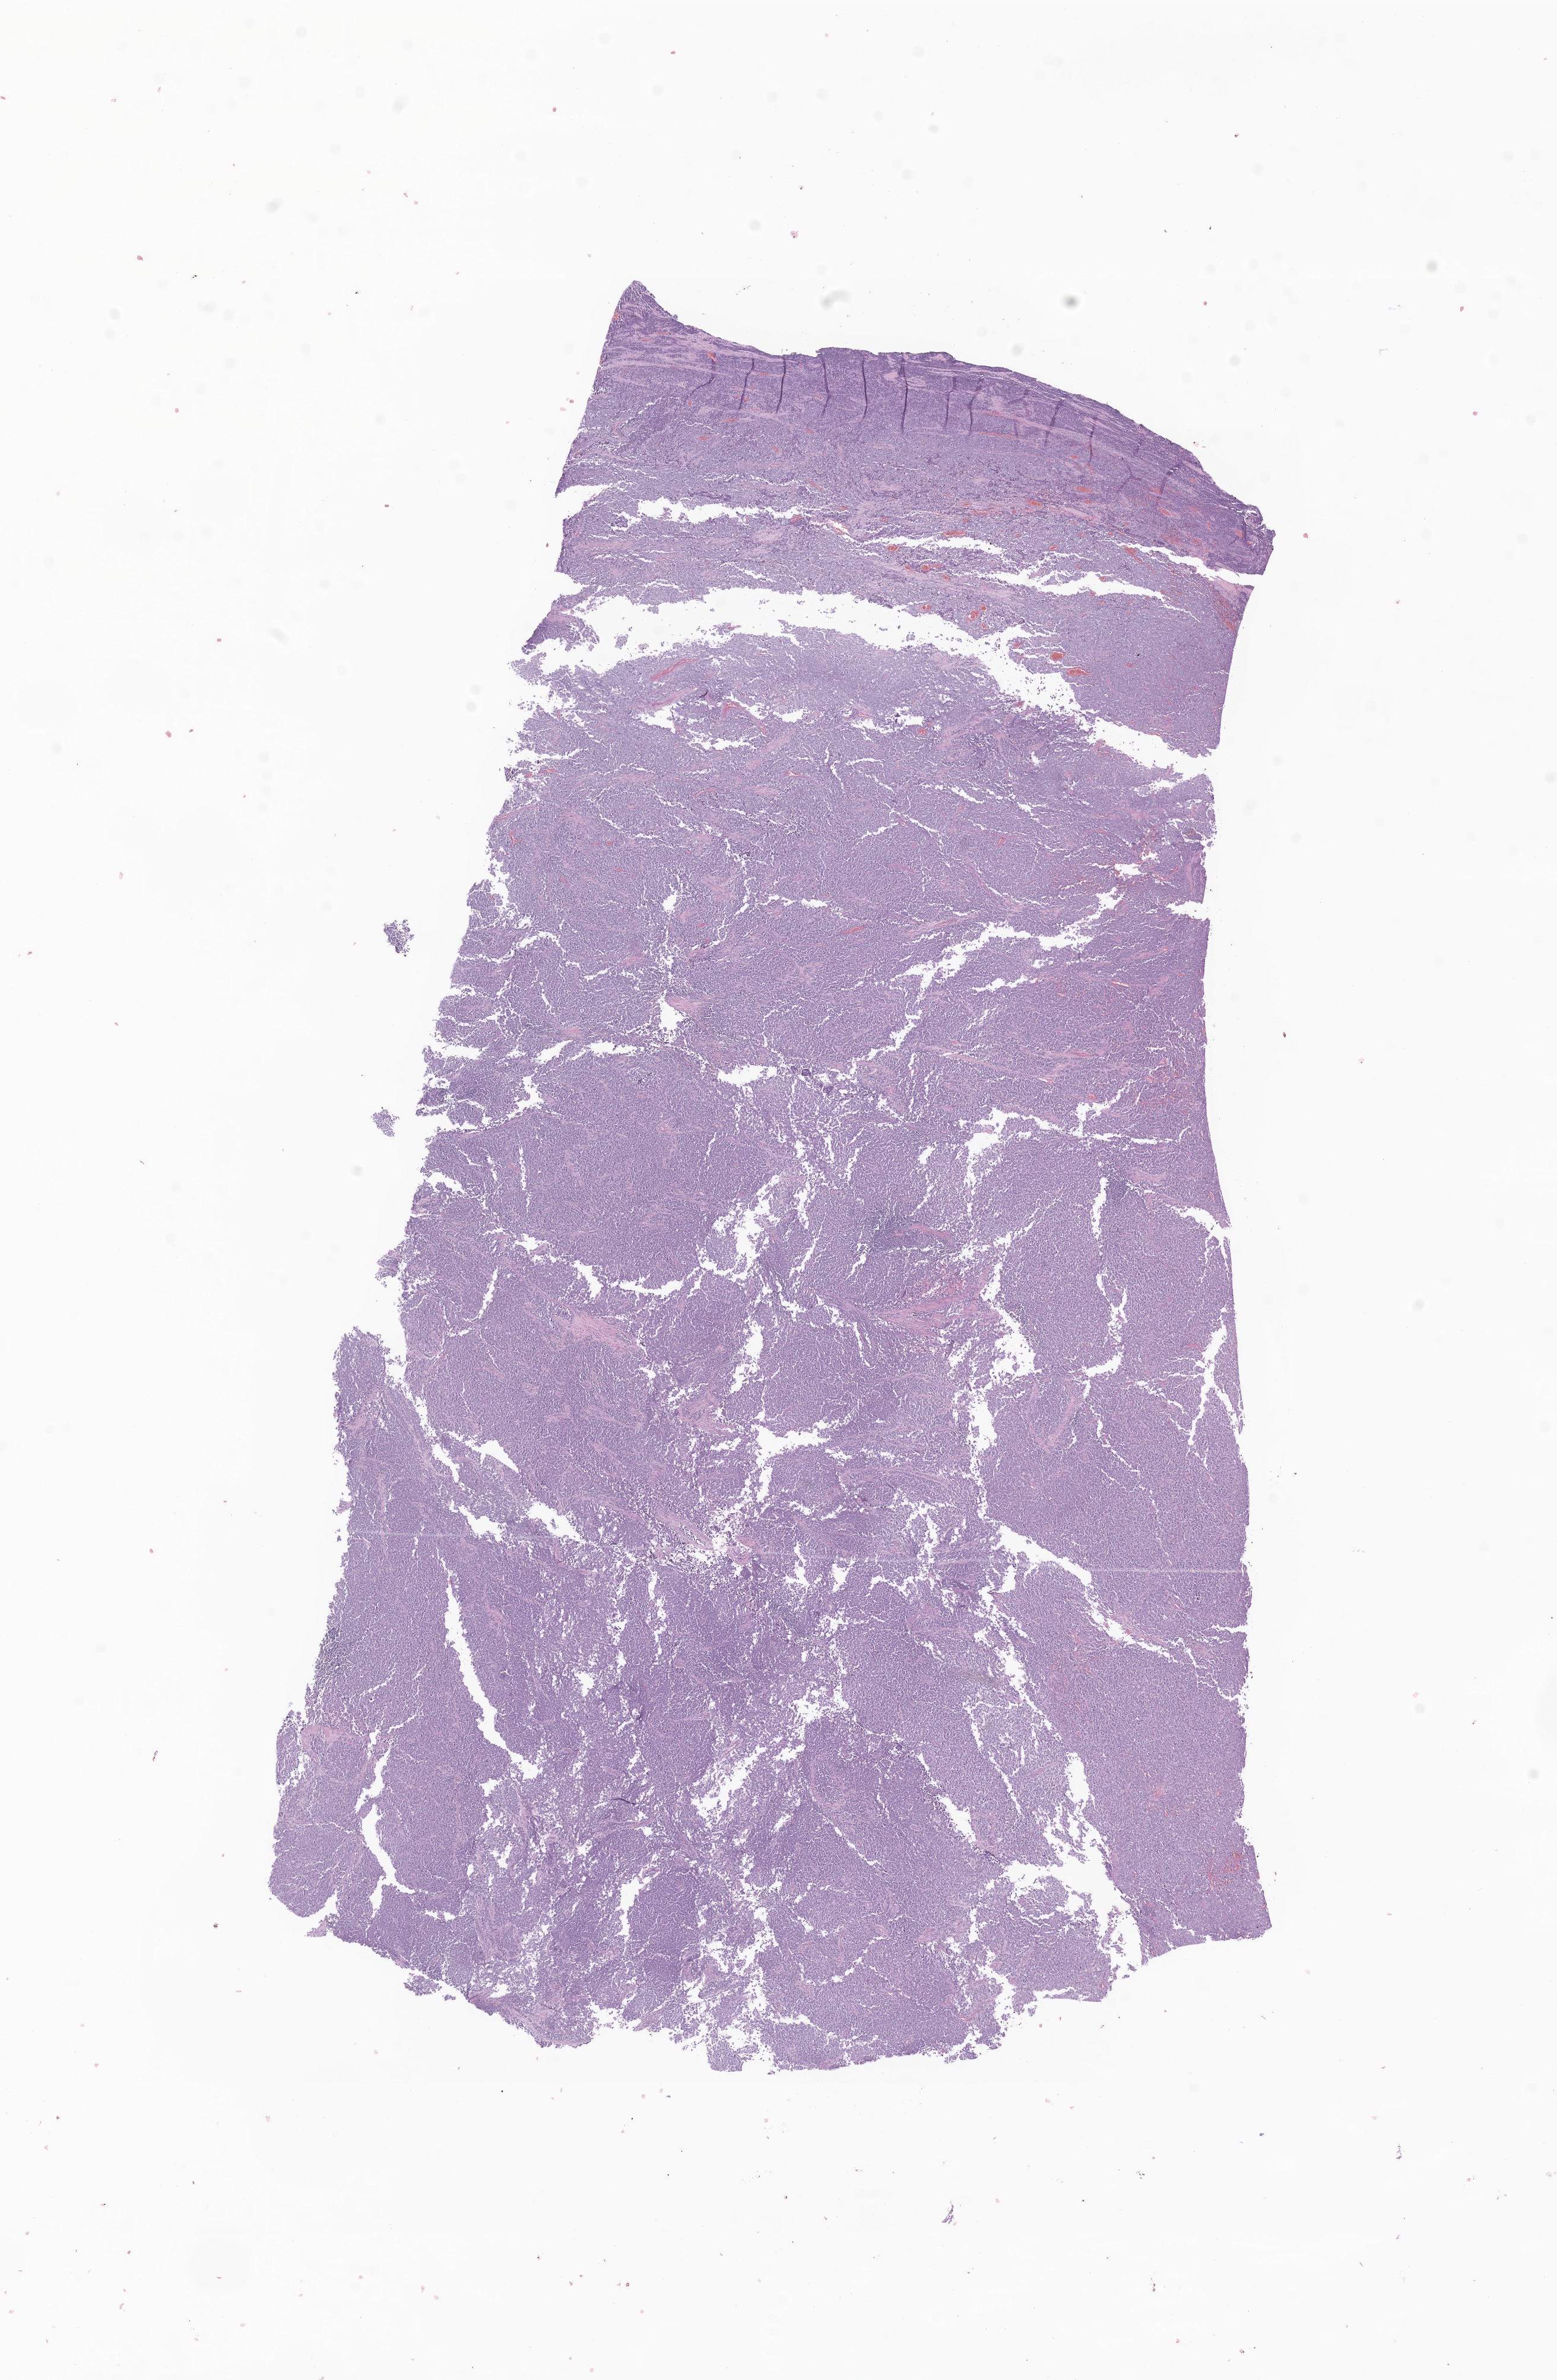
Whole-slide image, hematoxylin and eosin (H&E) stain of tumor tissue from the pelvis, a low-resolution overview of the entire scanned area, about 11.1 x 16.9 mm, formalin-fixed paraffin-embedded section. Male patient, age 221 months (18 years 5 months).
* diagnosis (ICD-O-3 morphology term): Alveolar rhabdomyosarcoma